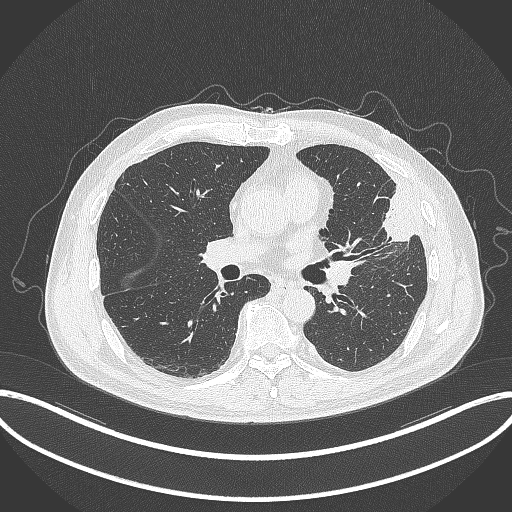
Chest CT, one axial slice; position 177 of 382 along the scan axis; 120 kVp; lung window (W 1500 / L -600 HU); 1 mm slice thickness; 512 × 512 image matrix, field of view 415 × 415 mm. Male patient, age 64 years. Case-level facts recorded for this patient, not image findings: clinical TNM (as recorded): T4 N1 M0; histopathological grade: G3.
Structures marked on this image (rectangle marked by the reading radiologist):
- lung tumour (recorded histology: adenocarcinoma): bounding box (x1, y1, x2, y2) in pixels: (367, 179, 419, 245)